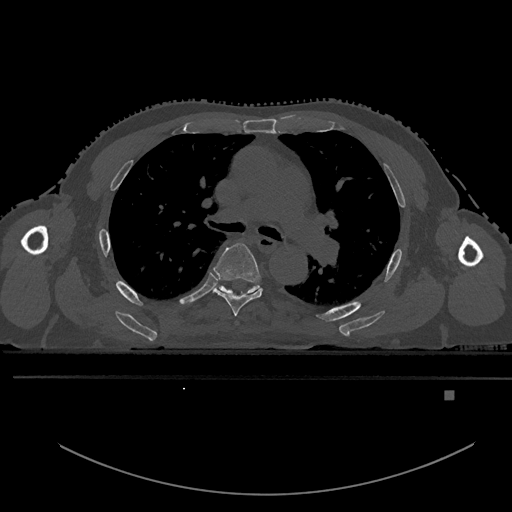
CT including the spine, one axial slice; position 348 of 969 along the scan axis; bone window (W 1800 / L 400 HU); 0.5 mm slice thickness; 512 × 512 image matrix. Patient: male, 82 years. From the clinical record (not read from this slice): primary cancer: prostate.
Annotated regions visible in this slice (semi-automatically segmented with operator editing):
- T5 vertebra: bounding box <213,242,263,316> (left, top, right, bottom; pixels)
- T6 vertebra: <214,284,260,296>